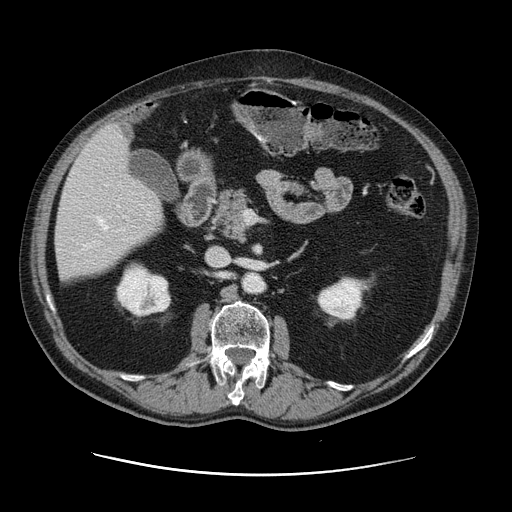
Contrast-enhanced abdominal CT, one axial slice. Position 58 of 141 along the scan axis. Intravenous contrast given. Soft-tissue window (W 400 / L 40 HU). 2.5 mm slice thickness. 512 × 512 image matrix, field of view 395 × 395 mm. Male patient, age 72 years. Case-level facts recorded for this patient, not image findings: diagnosis: colorectal cancer liver metastases, imaged before liver resection; multiple liver metastases: yes; largest metastasis: 5.4 cm.
Annotated regions visible in this slice (expert manual segmentation):
- hepatic veins: bounding box <98,217,108,230> (left, top, right, bottom; pixels)
- liver: <56,126,164,281>
- planned liver remnant (the part of the liver to remain after resection): <56,182,164,282>
- portal vein (with intrahepatic branches): <98,205,120,243>